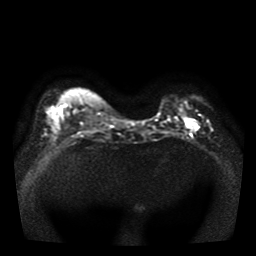
Breast MRI, one axial slice; position 12 of 41 along the scan axis; diffusion-weighted series; image 2 of 4 stored at this slice position (different b-values; order by instance number); 1.5 T; 5 mm slice thickness; 256 × 256 image matrix, field of view 330 × 330 mm. Female patient.
Annotated regions visible in this slice (outlined manually by an expert reader):
- tumour on diffusion-weighted imaging: bounding box (x1, y1, x2, y2) in pixels: (184, 121, 198, 130)